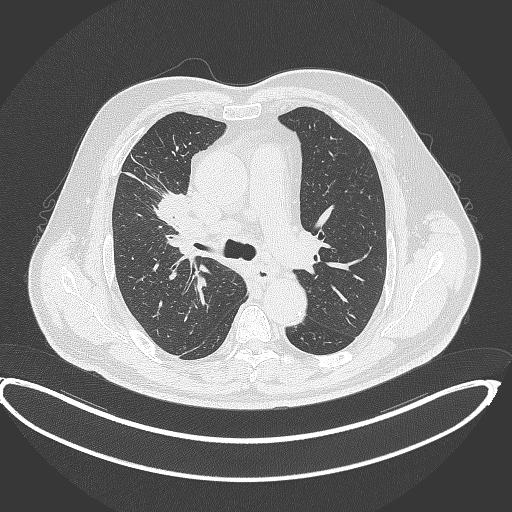
Chest CT, one axial slice. Slice 267 of 390 in the series (ordered by position). Reconstruction kernel B70f. Lung window (W 1500 / L -600 HU). 1 mm slice thickness. 512 × 512 image matrix, field of view 448 × 448 mm. Patient: male, 62 years. From the clinical record (not read from this slice): clinical TNM (as recorded): T1c N3 M1c.
Annotated regions visible in this slice (bounding box drawn by a radiologist):
- lung tumour (recorded histology: adenocarcinoma): bounding box <156,191,197,234> (left, top, right, bottom; pixels)